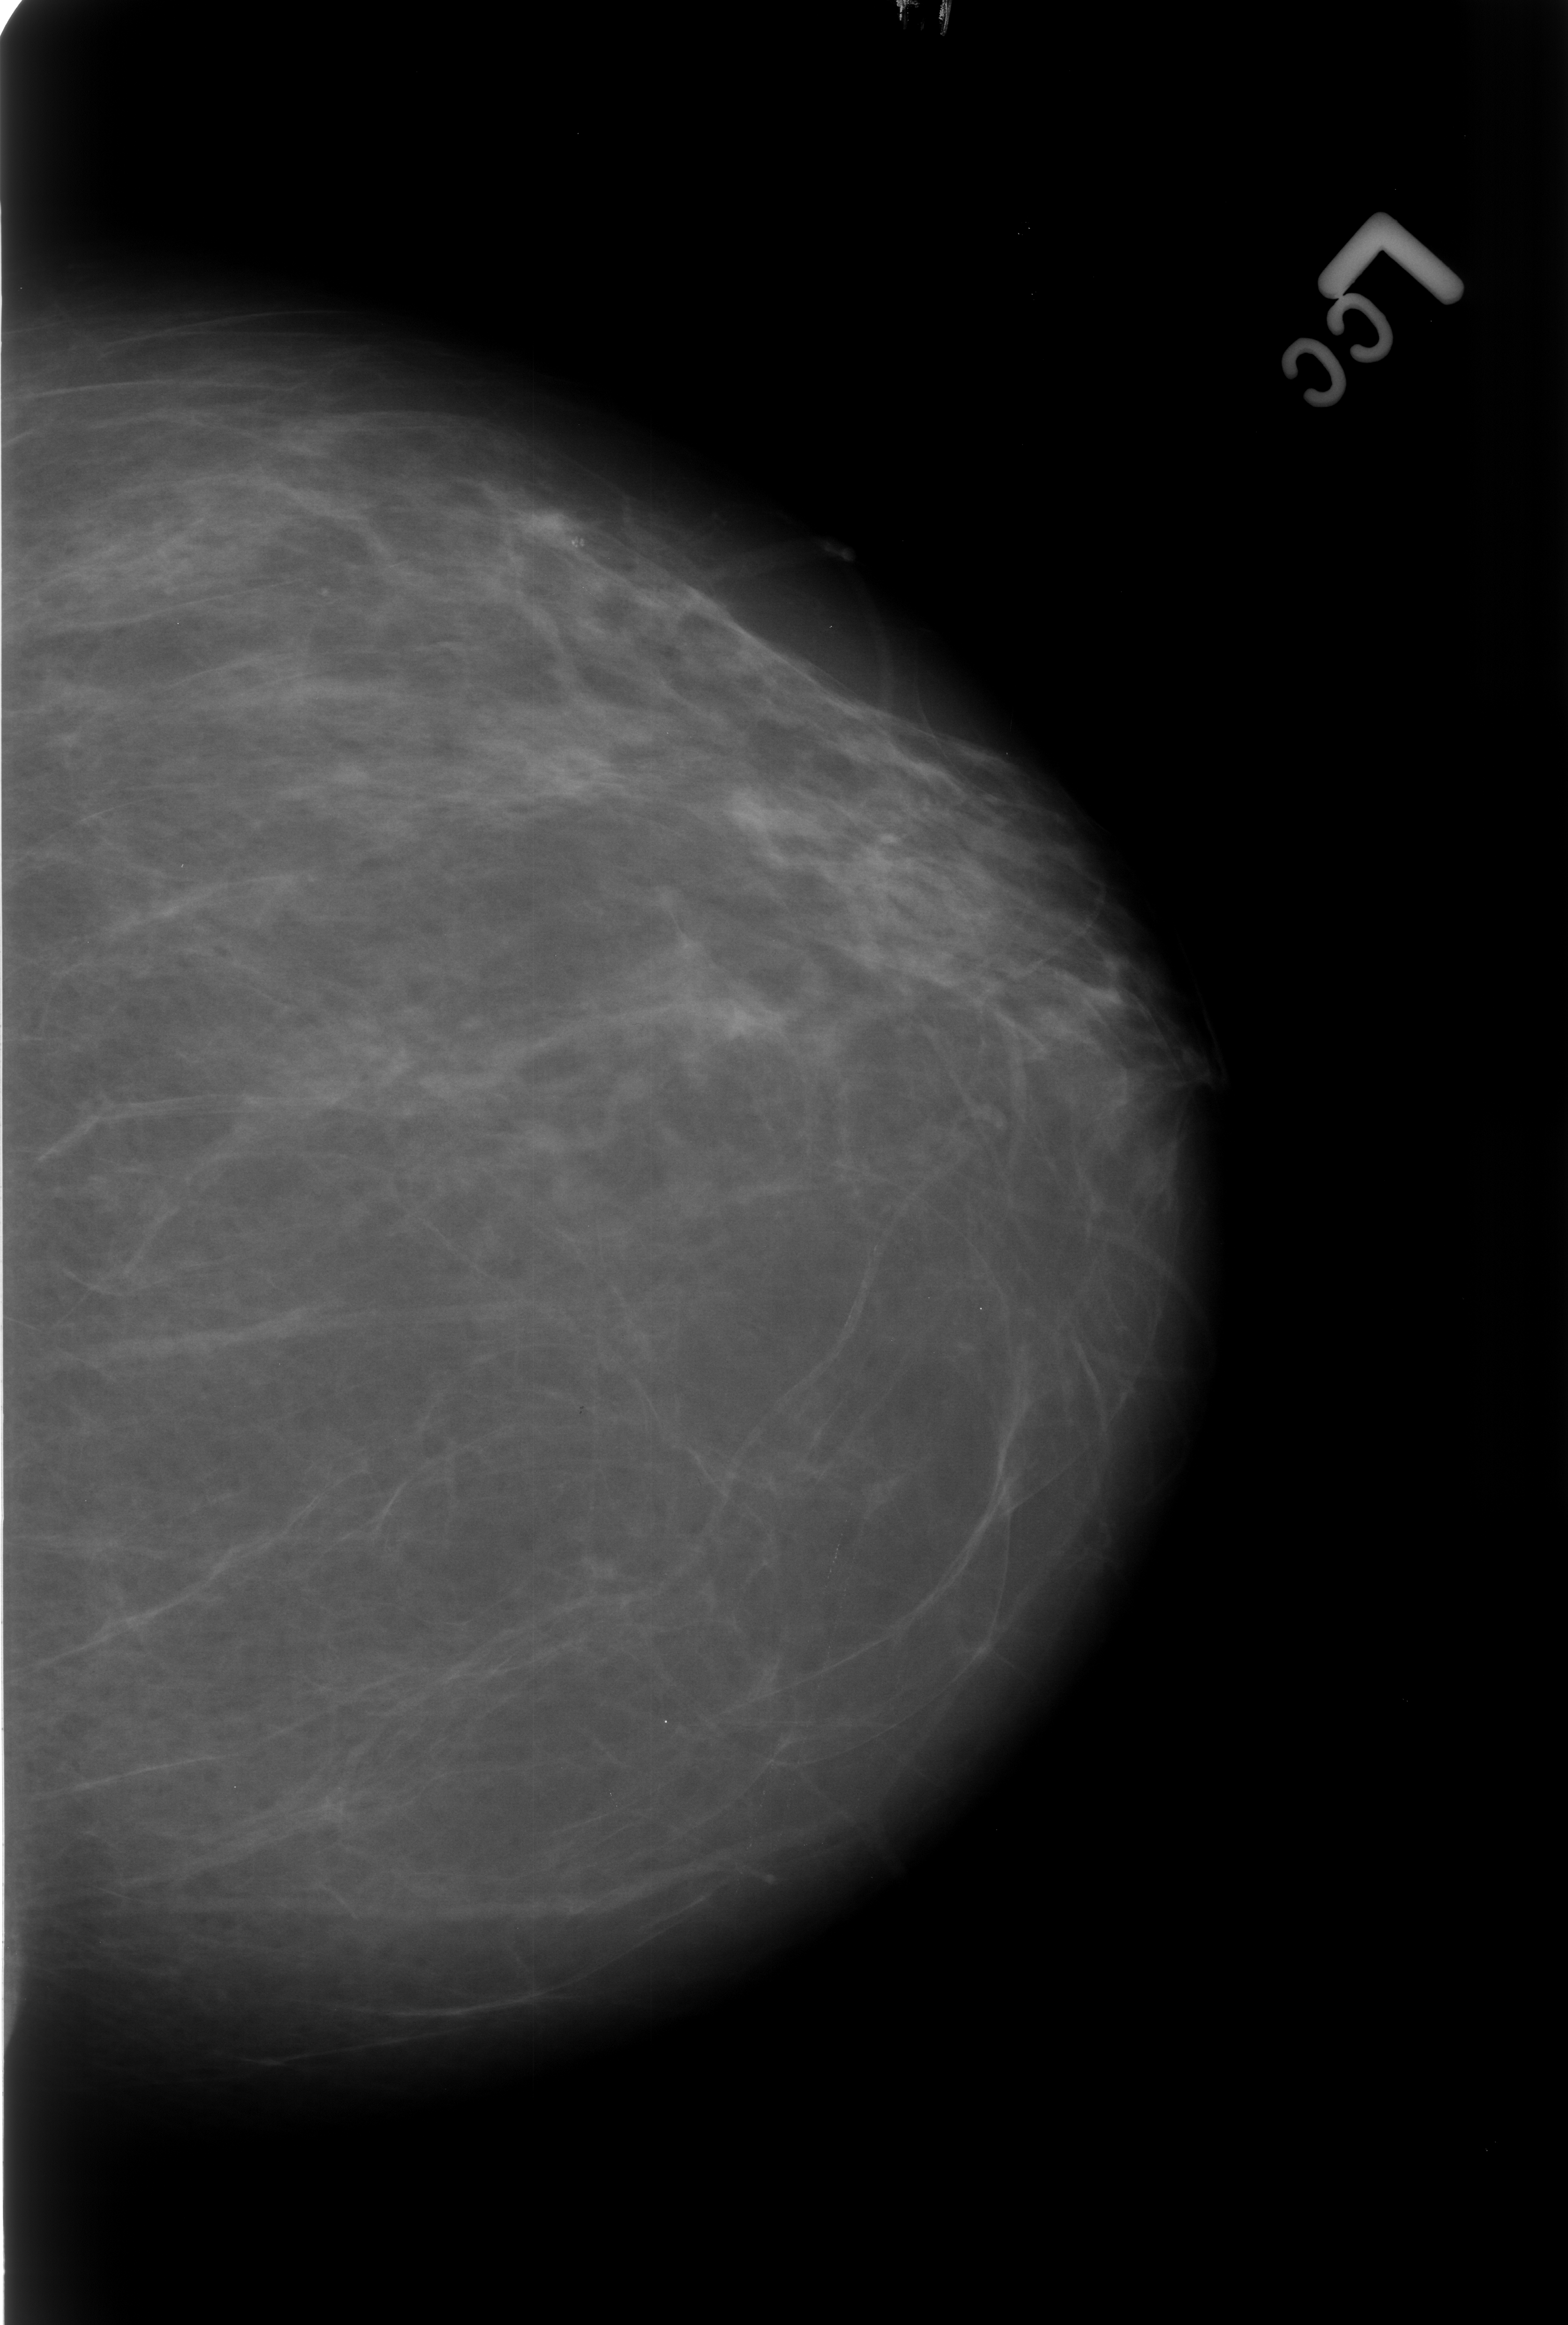
Mammogram (digitized film); left breast; CC view; BI-RADS breast density category 2 (scale 1–4).
Marked findings (only marked abnormalities are described; nothing is implied about the rest of the image): calcifications, morphology punctate / pleomorphic, distribution clustered; BI-RADS assessment category 4; pathology result (as recorded, not read from the image): benign.